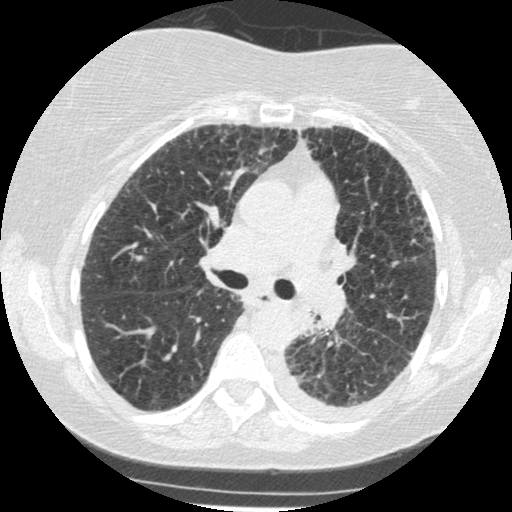
Low-dose screening chest CT, one axial slice; reconstruction kernel STANDARD; 120 kVp; lung window (W 1500 / L -600 HU); 1.25 mm slice thickness; 512 × 512 image matrix, field of view 310 × 310 mm.
Structures marked on this image (expert manual segmentation):
- lesion 1 (tumor, lower lobe of left lung): bounding box [x1, y1, x2, y2] px = [295, 308, 315, 335]